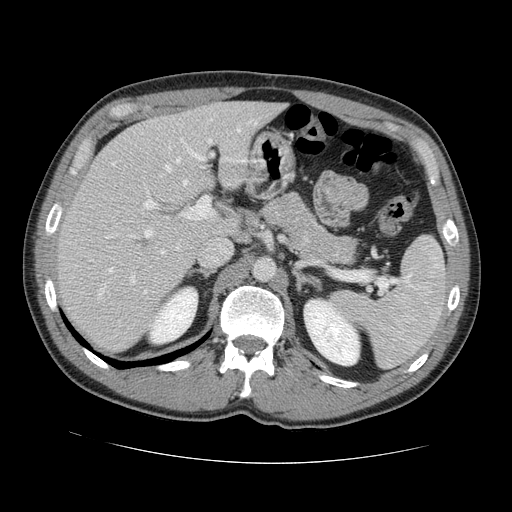
Contrast-enhanced abdominal CT, one axial slice; position 86 of 131 along the scan axis; 120 kVp; soft-tissue window (W 400 / L 40 HU); 2.5 mm slice thickness; 512 × 512 image matrix. Male patient, age 40 years. From the clinical record (not read from this slice): diagnosis: colorectal cancer liver metastases, imaged before liver resection; multiple liver metastases: yes; largest metastasis: 2.9 cm; disease in both lobes: yes.
Structures marked on this image (manually delineated by an expert):
- hepatic veins: bounding box [x1, y1, x2, y2] px = [98, 157, 187, 298]
- liver: [60, 102, 281, 352]
- planned liver remnant (the part of the liver to remain after resection): [102, 103, 281, 236]
- portal vein (with intrahepatic branches): [105, 151, 212, 284]
- liver metastasis: [135, 240, 151, 248]